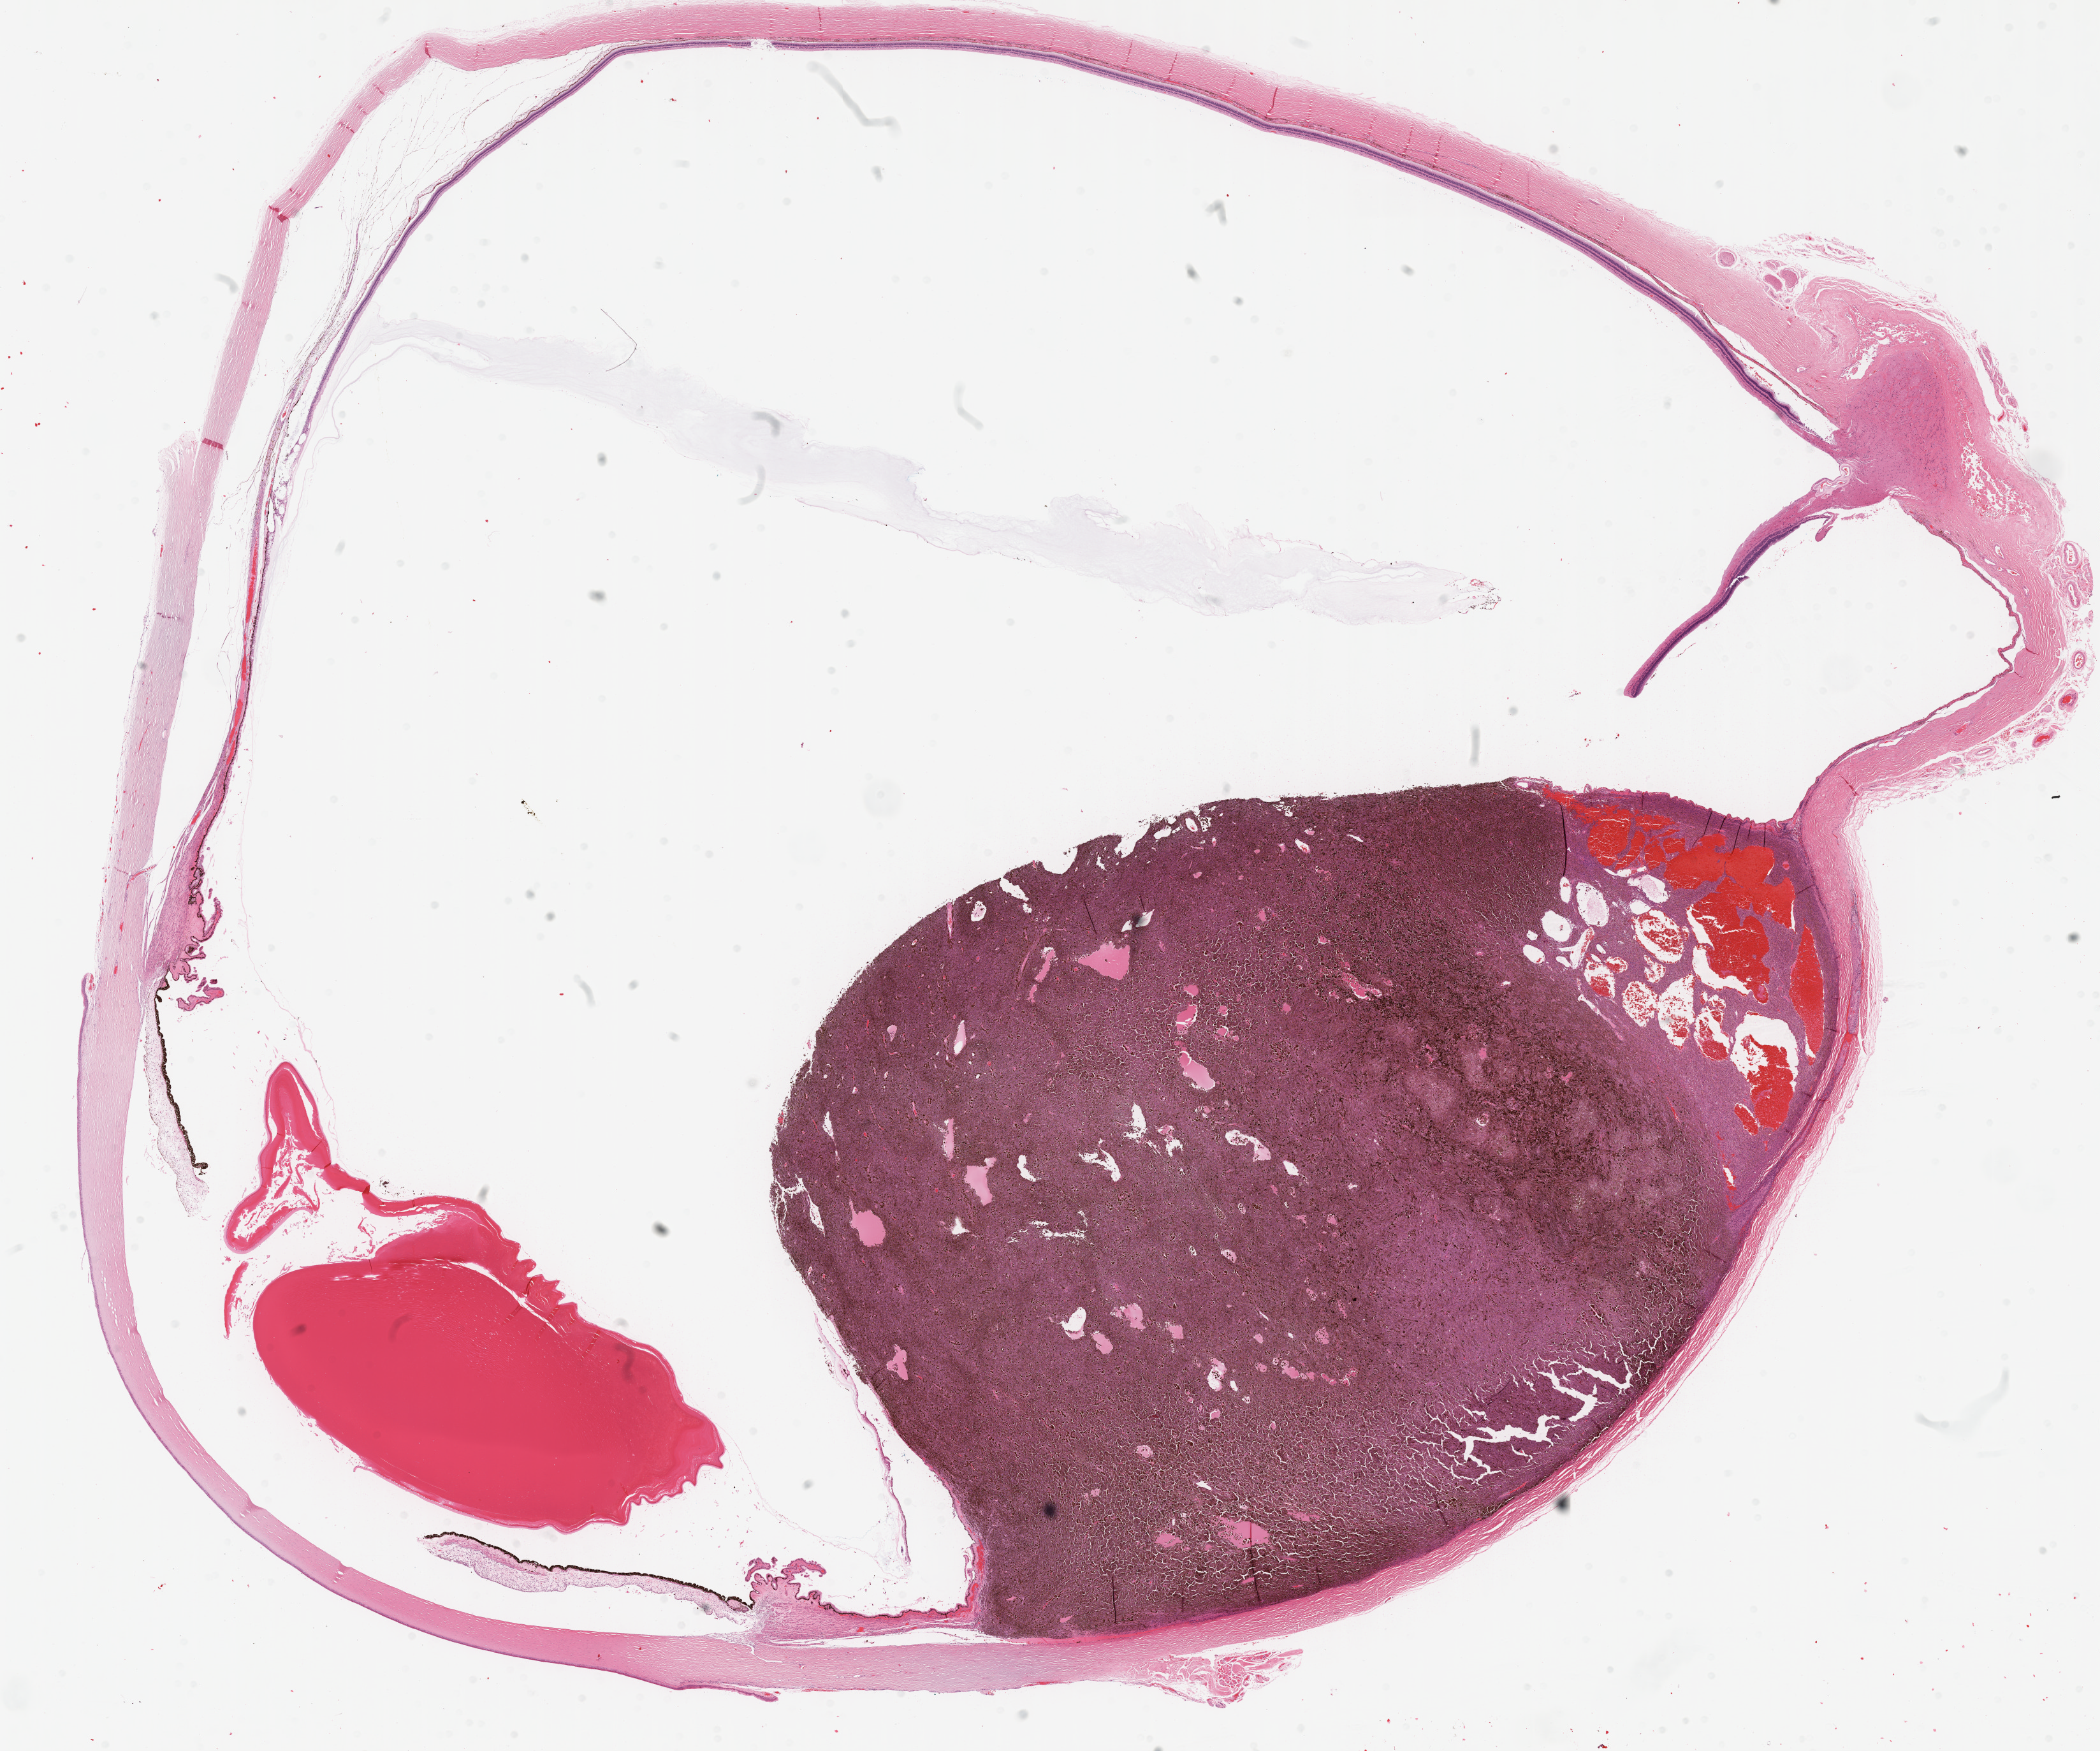
Digitized H&E-stained tissue section (whole slide) — shown as a low-resolution overview of the whole scanned area (about 26.6 x 22.1 mm, slide scanned at 20x). Formalin-fixed paraffin-embedded (FFPE) diagnostic section. Uvea, primary tumour sample. Patient: male, age at initial diagnosis 77 years.
* TNM: T3a N0 M0
* AJCC pathologic stage: IIB
* histologic diagnosis: Mixed epithelioid and spindle cell melanoma (choroid)